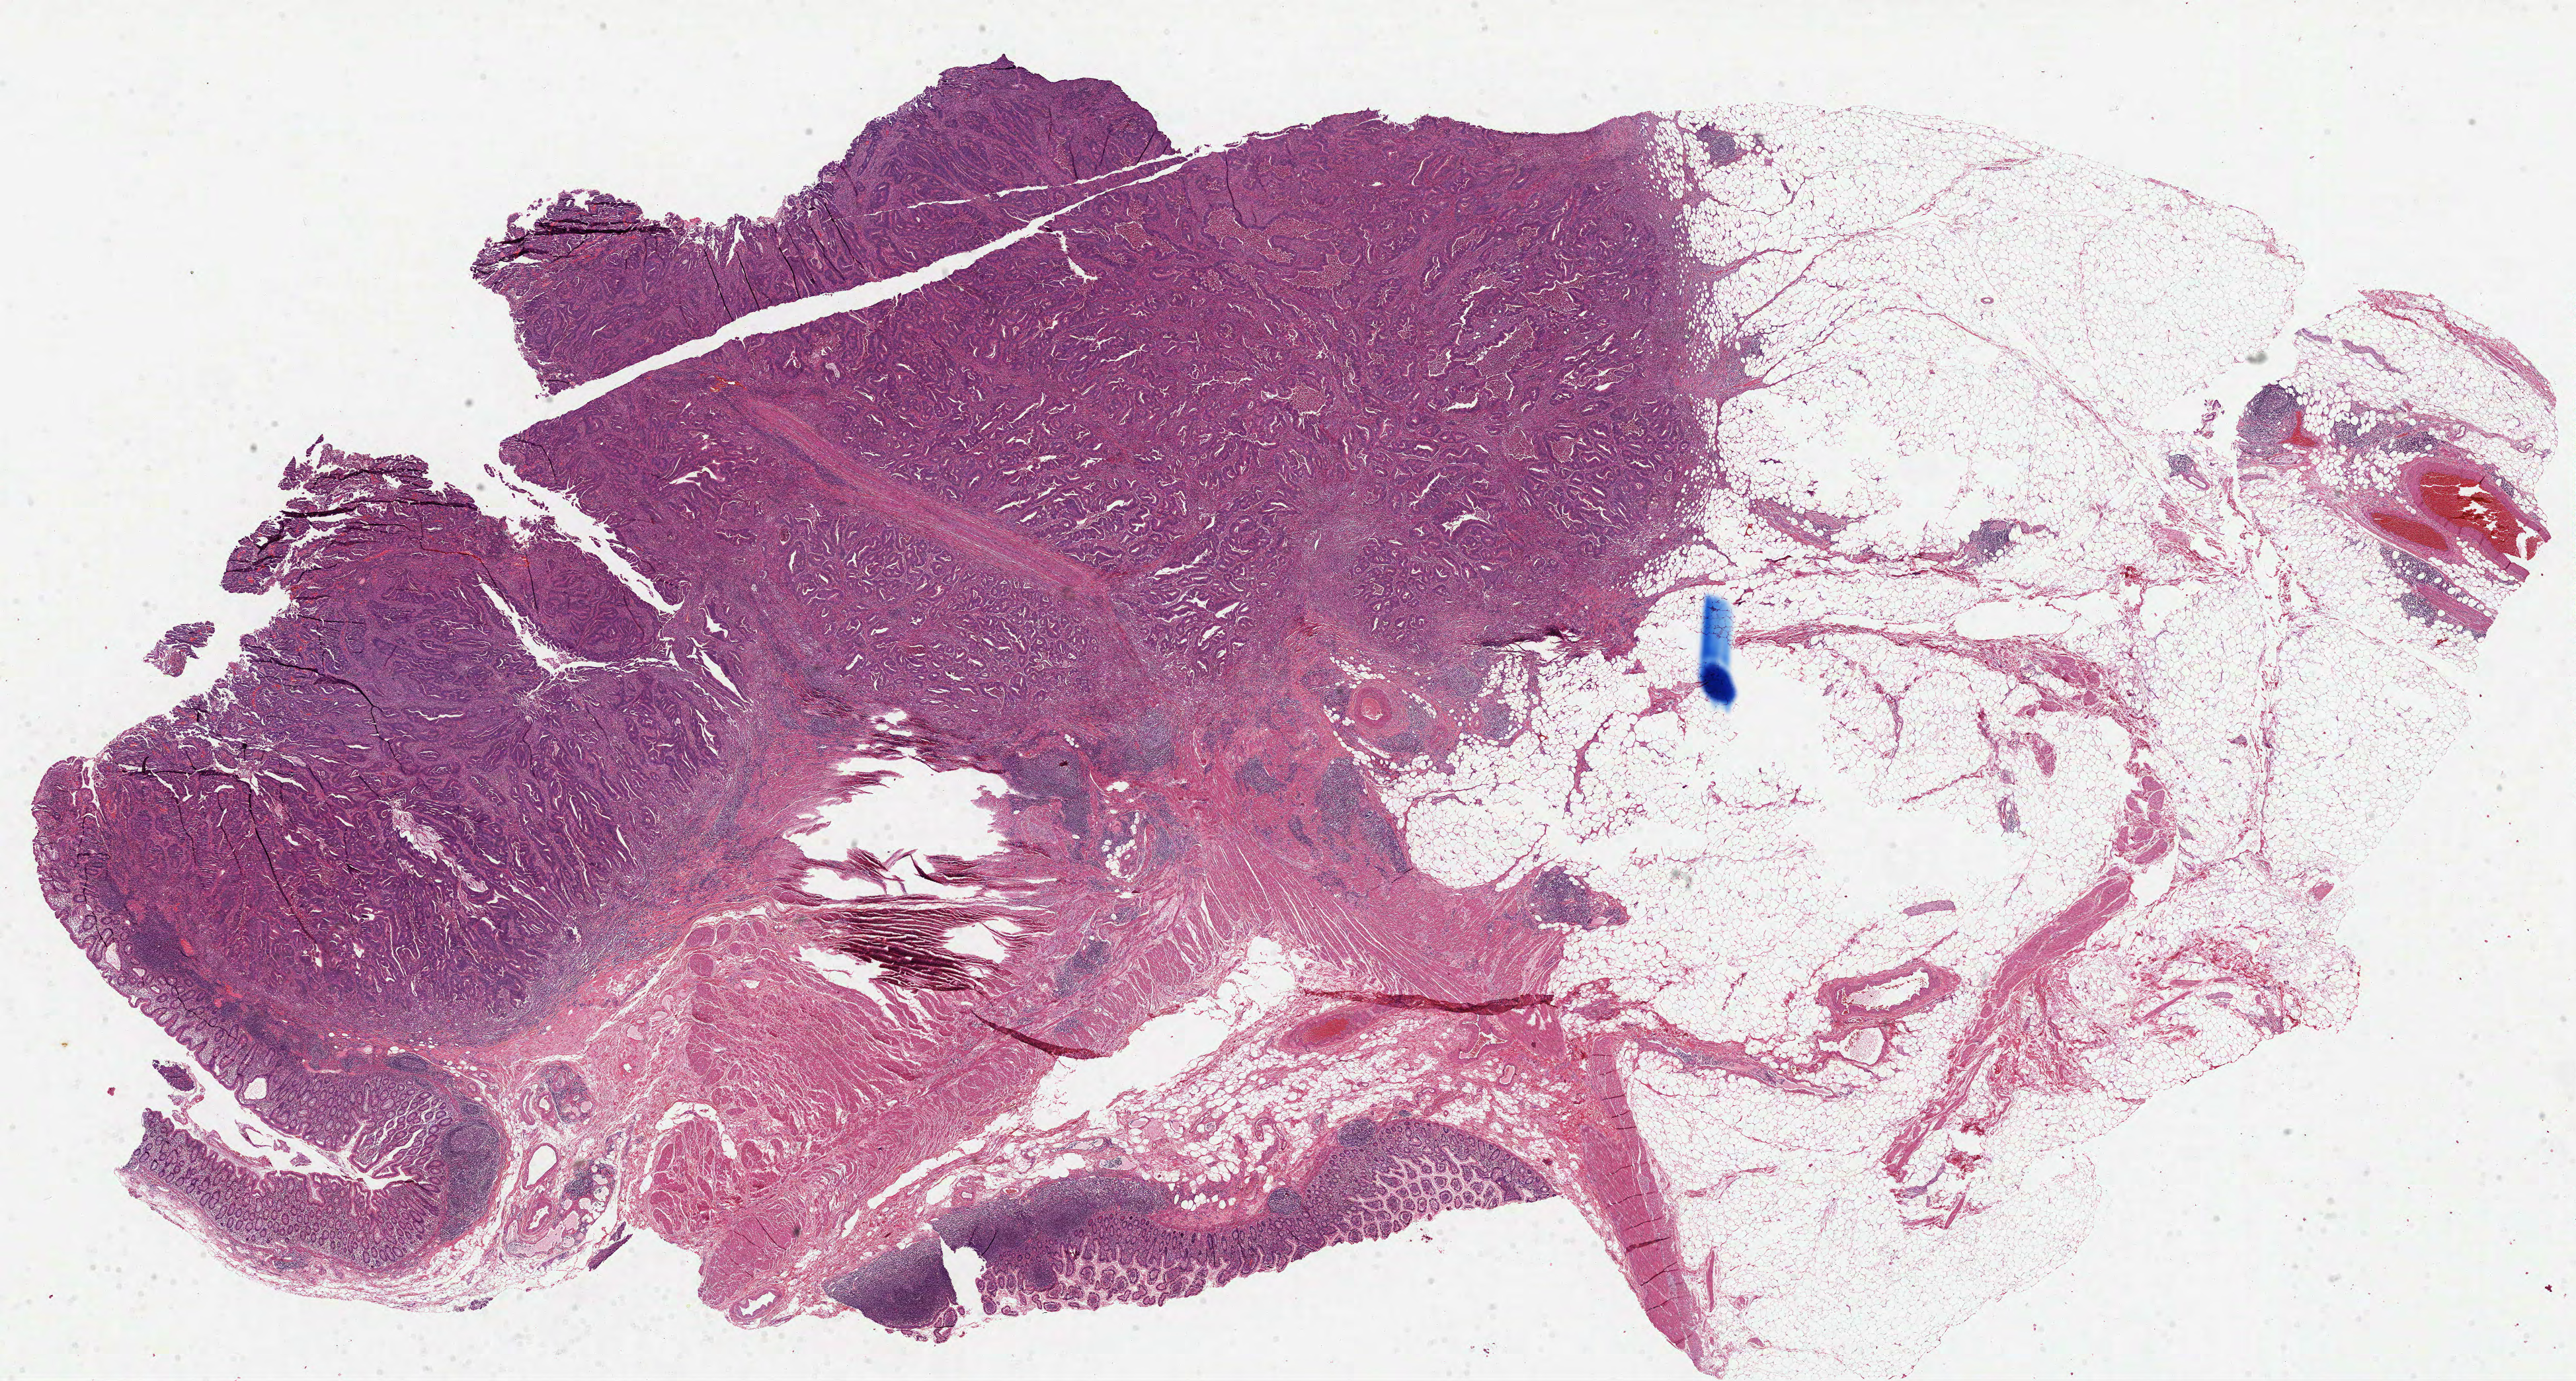
Hematoxylin and eosin (H&E) stained whole-slide image — shown as a low-resolution overview of the whole scanned area (about 31.4 x 16.8 mm, acquisition: 40x scan), formalin-fixed paraffin-embedded (FFPE) diagnostic section, primary tumour sample from the colon. Patient: male, age at initial diagnosis 61 years.
Pathologic diagnosis: Adenocarcinoma, NOS (cecum).